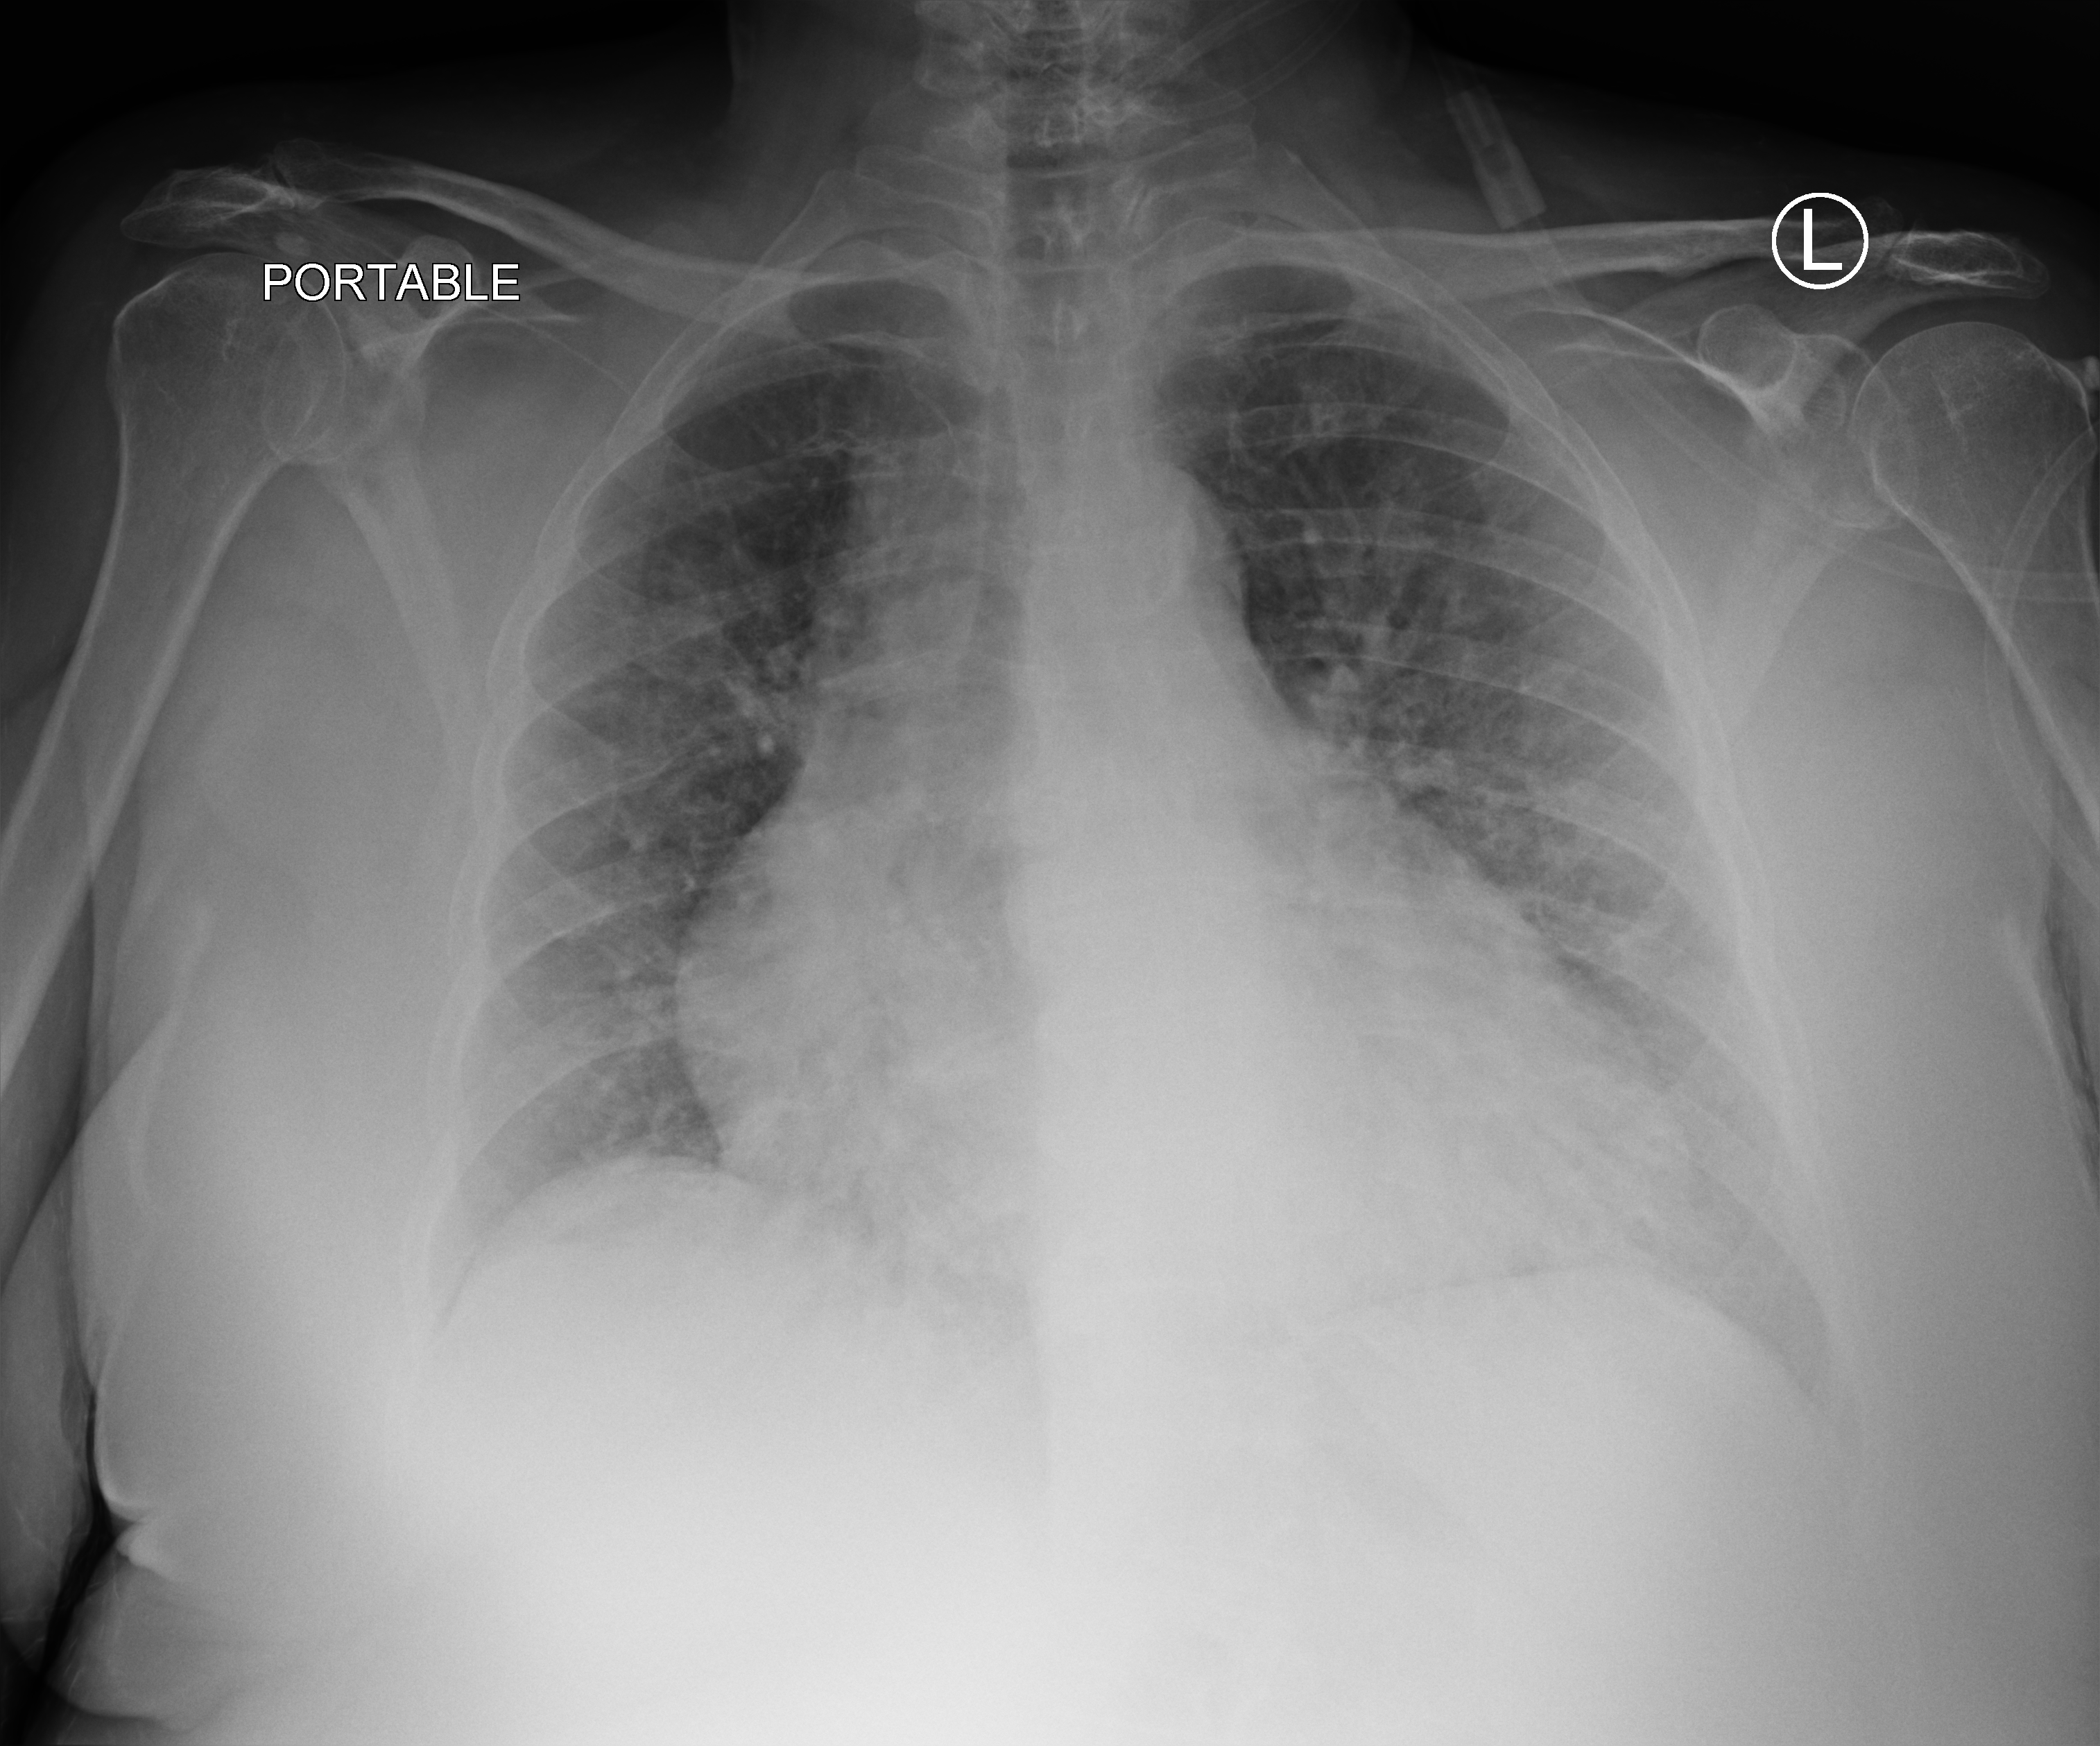
Chest X-ray (portable); anteroposterior (AP) projection. Female patient hospitalised with COVID-19, age 75–90 years.
Admission-level facts for this patient (not findings on this image; timing relative to this image not recorded): mechanically ventilated during this hospital stay: yes; admitted to intensive care during this hospital stay: yes.